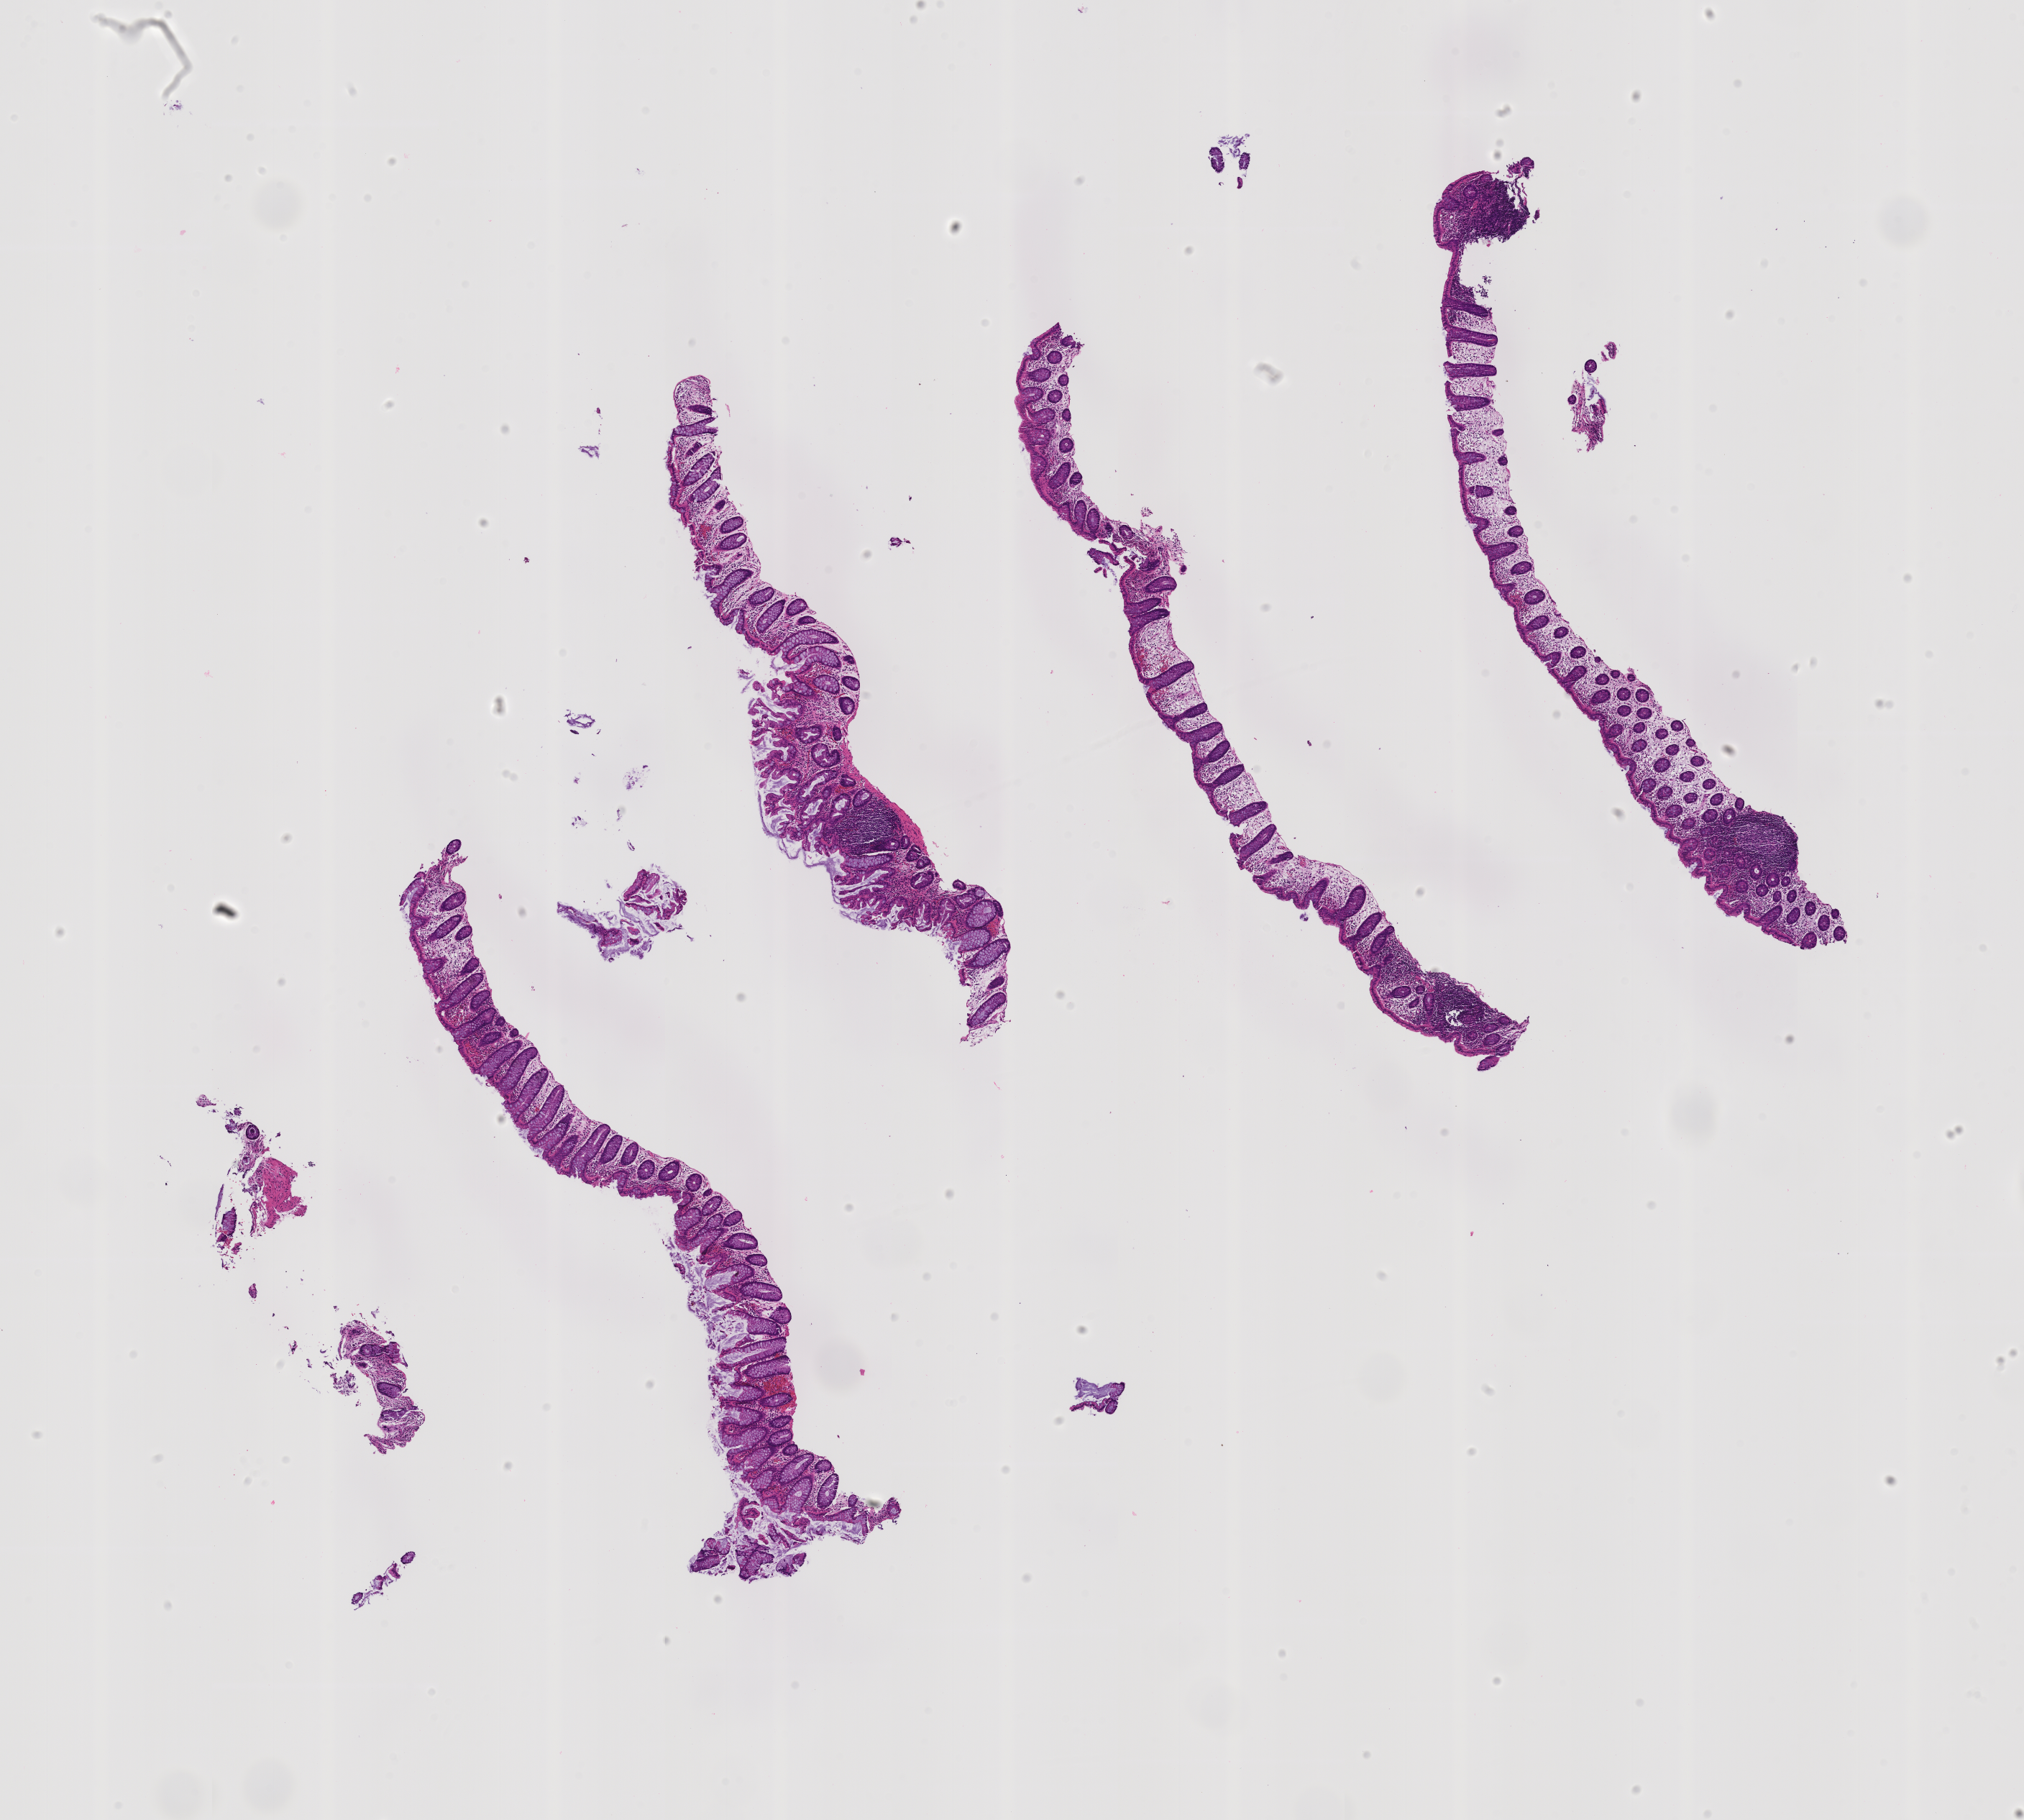
Hematoxylin and eosin (H&E) whole-slide image of a colon biopsy — low-resolution overview of the scanned area, about 11.3 x 10.1 mm. Patient: female.
- specimen: formalin-fixed paraffin-embedded section; site: rectum